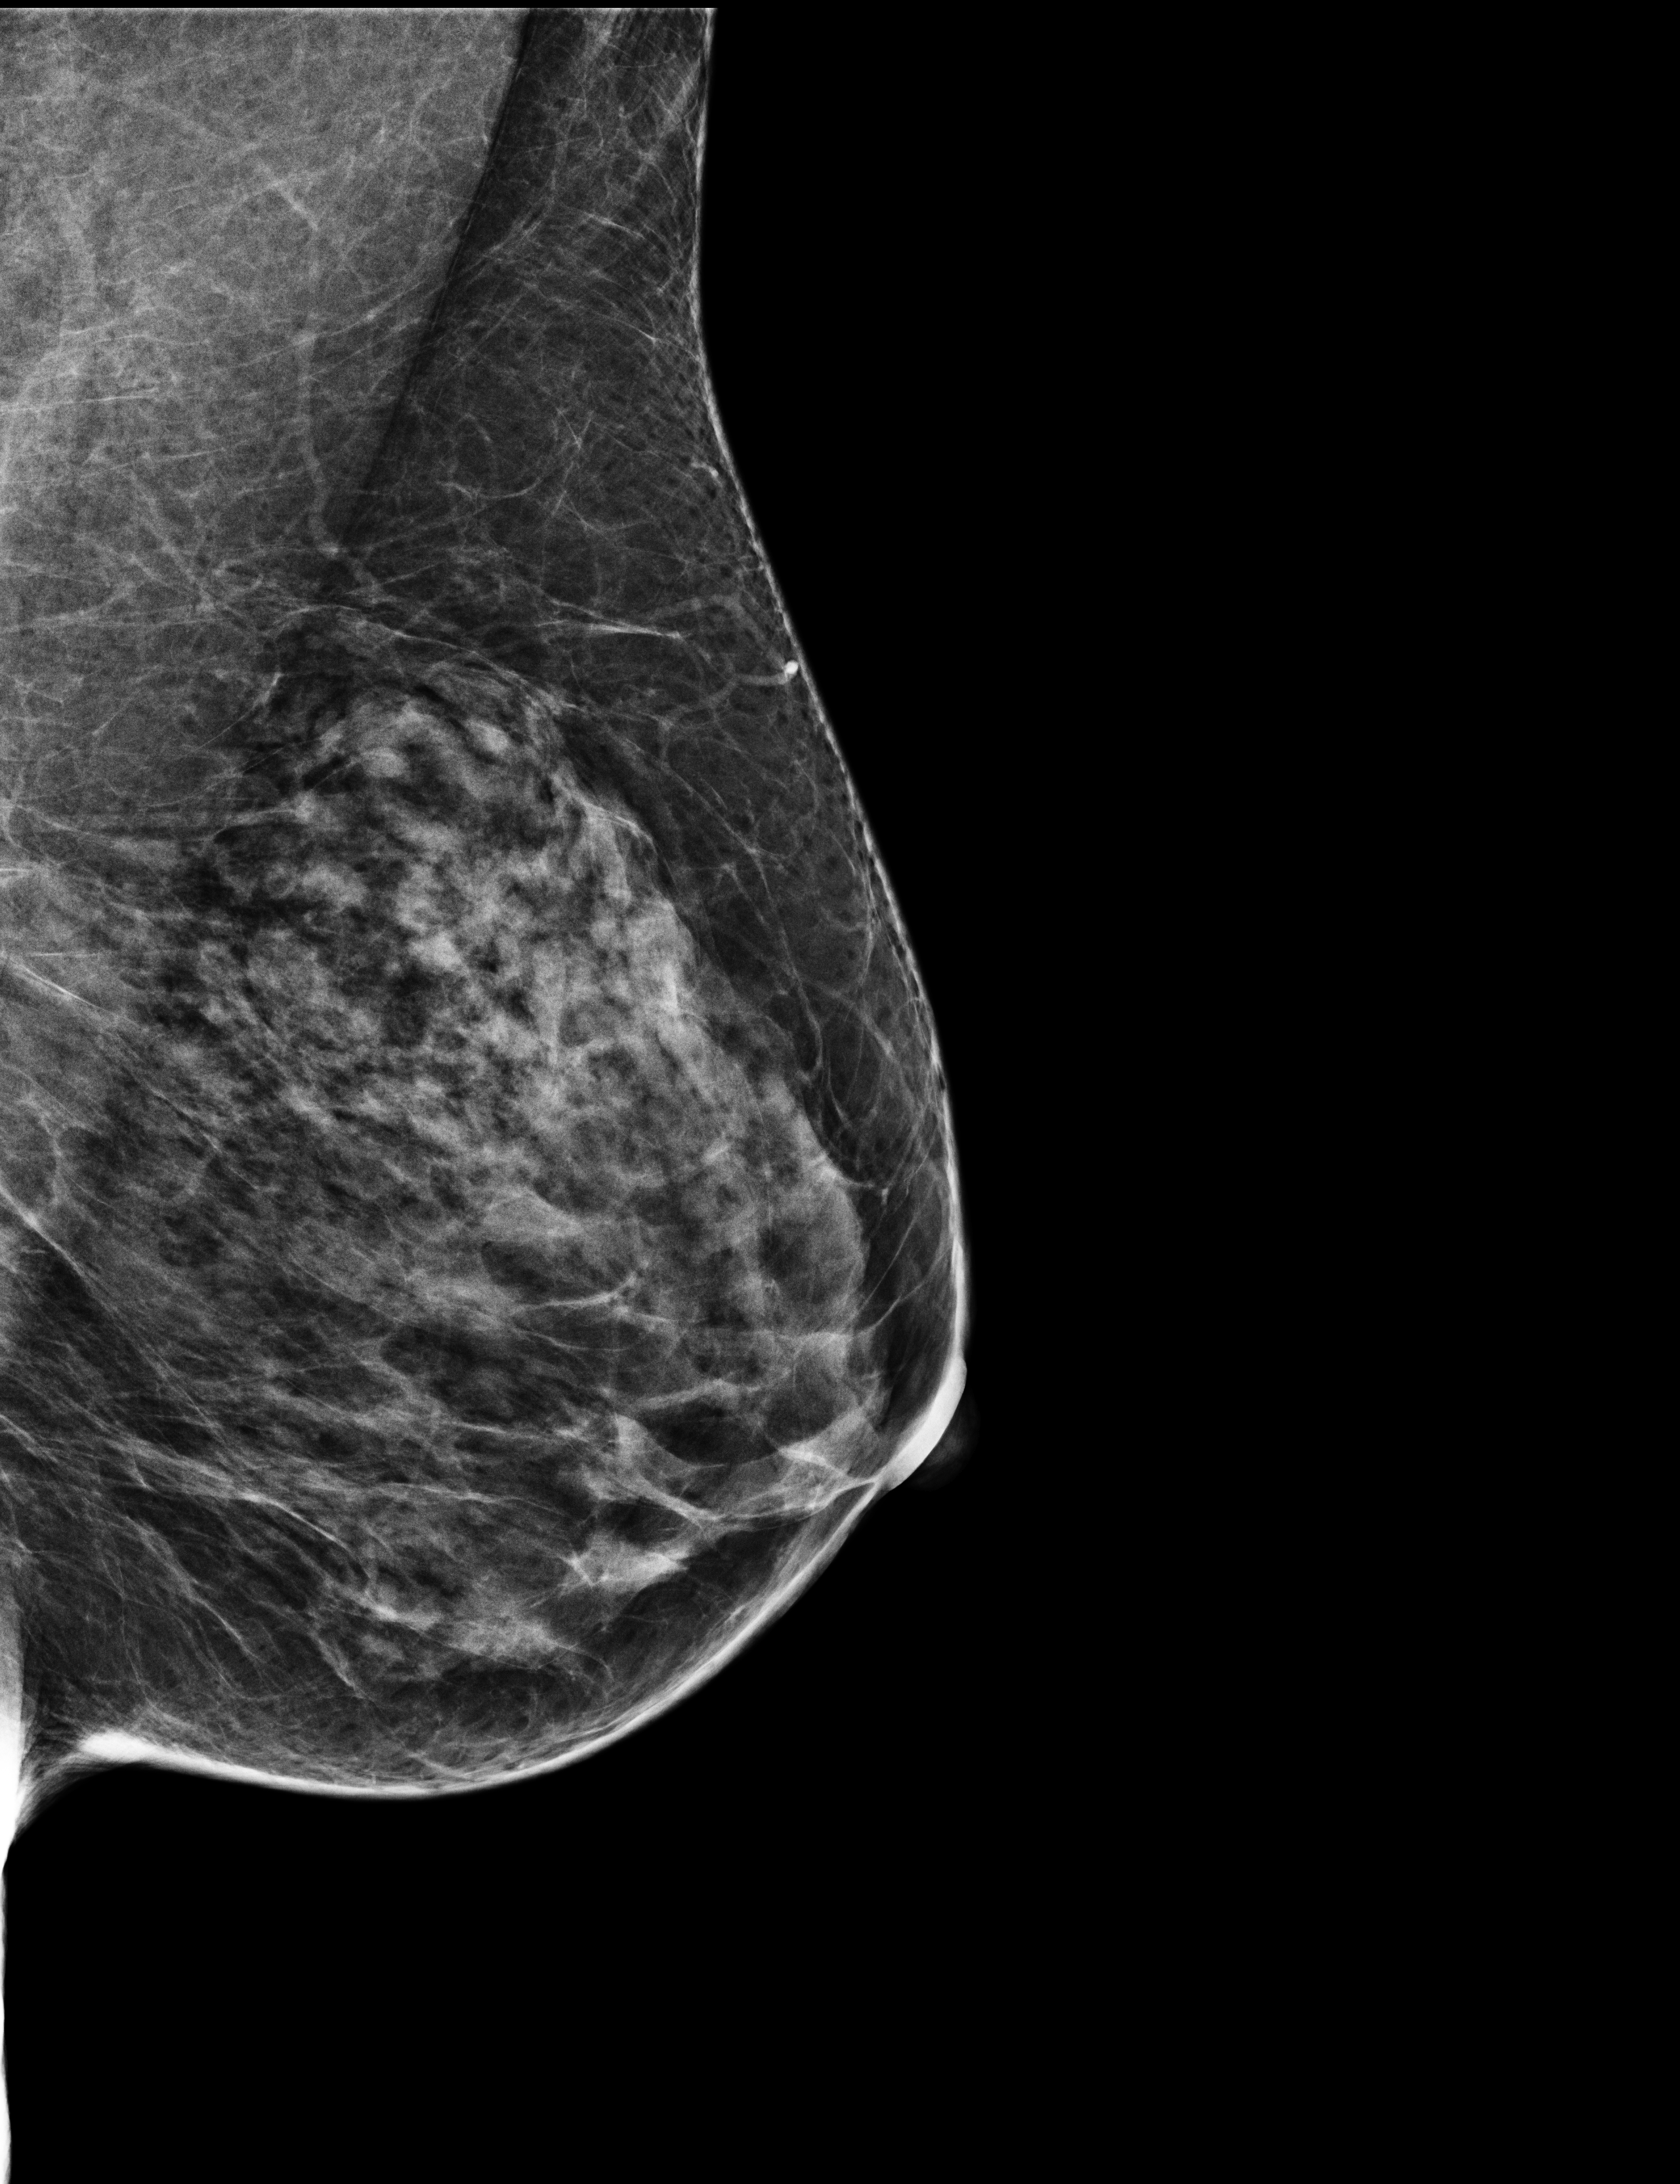
Screening examination; compressed breast thickness 41 mm. Female patient, age 67 years.
Image type: full-field digital mammogram. Breast: left. Projection: medio-lateral oblique projection.